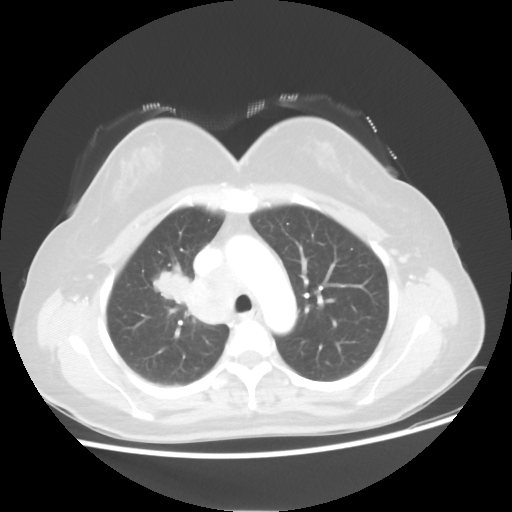
Chest CT, one axial slice. Slice 36 of 50 in the series (ordered by position). Reconstruction kernel STANDARD. Lung window (W 1500 / L -600 HU). 5 mm slice thickness. 512 × 512 image matrix, field of view 360 × 360 mm. Female patient, age 40 years. From the clinical record (not read from this slice): clinical TNM (as recorded): T1c N3 M0.
Structures marked on this image (bounding box drawn by a radiologist):
- lung tumour (recorded histology: small cell carcinoma): box from (x=154, y=265) to (x=187, y=314) px